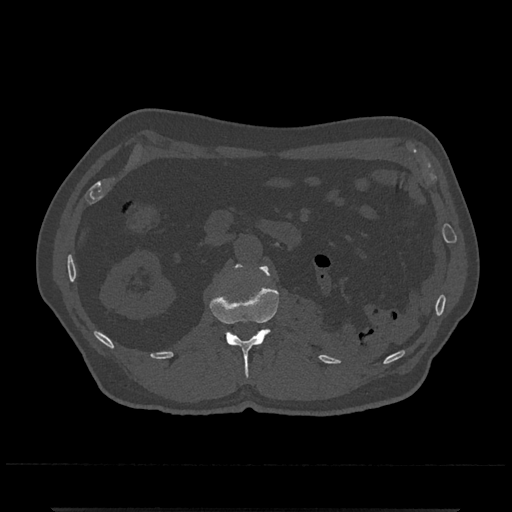
CT including the spine, one axial slice. Position 348 of 797 along the scan axis. Bone window (W 1800 / L 400 HU). 512 × 512 image matrix. Patient: male, 67 years. Case-level facts recorded for this patient, not image findings: primary cancer: prostate.
Annotated regions visible in this slice (semi-automatically segmented with operator editing):
- L1 vertebra: box from (x=210, y=264) to (x=279, y=378) px
- L2 vertebra: (x=239, y=265)–(x=243, y=267)